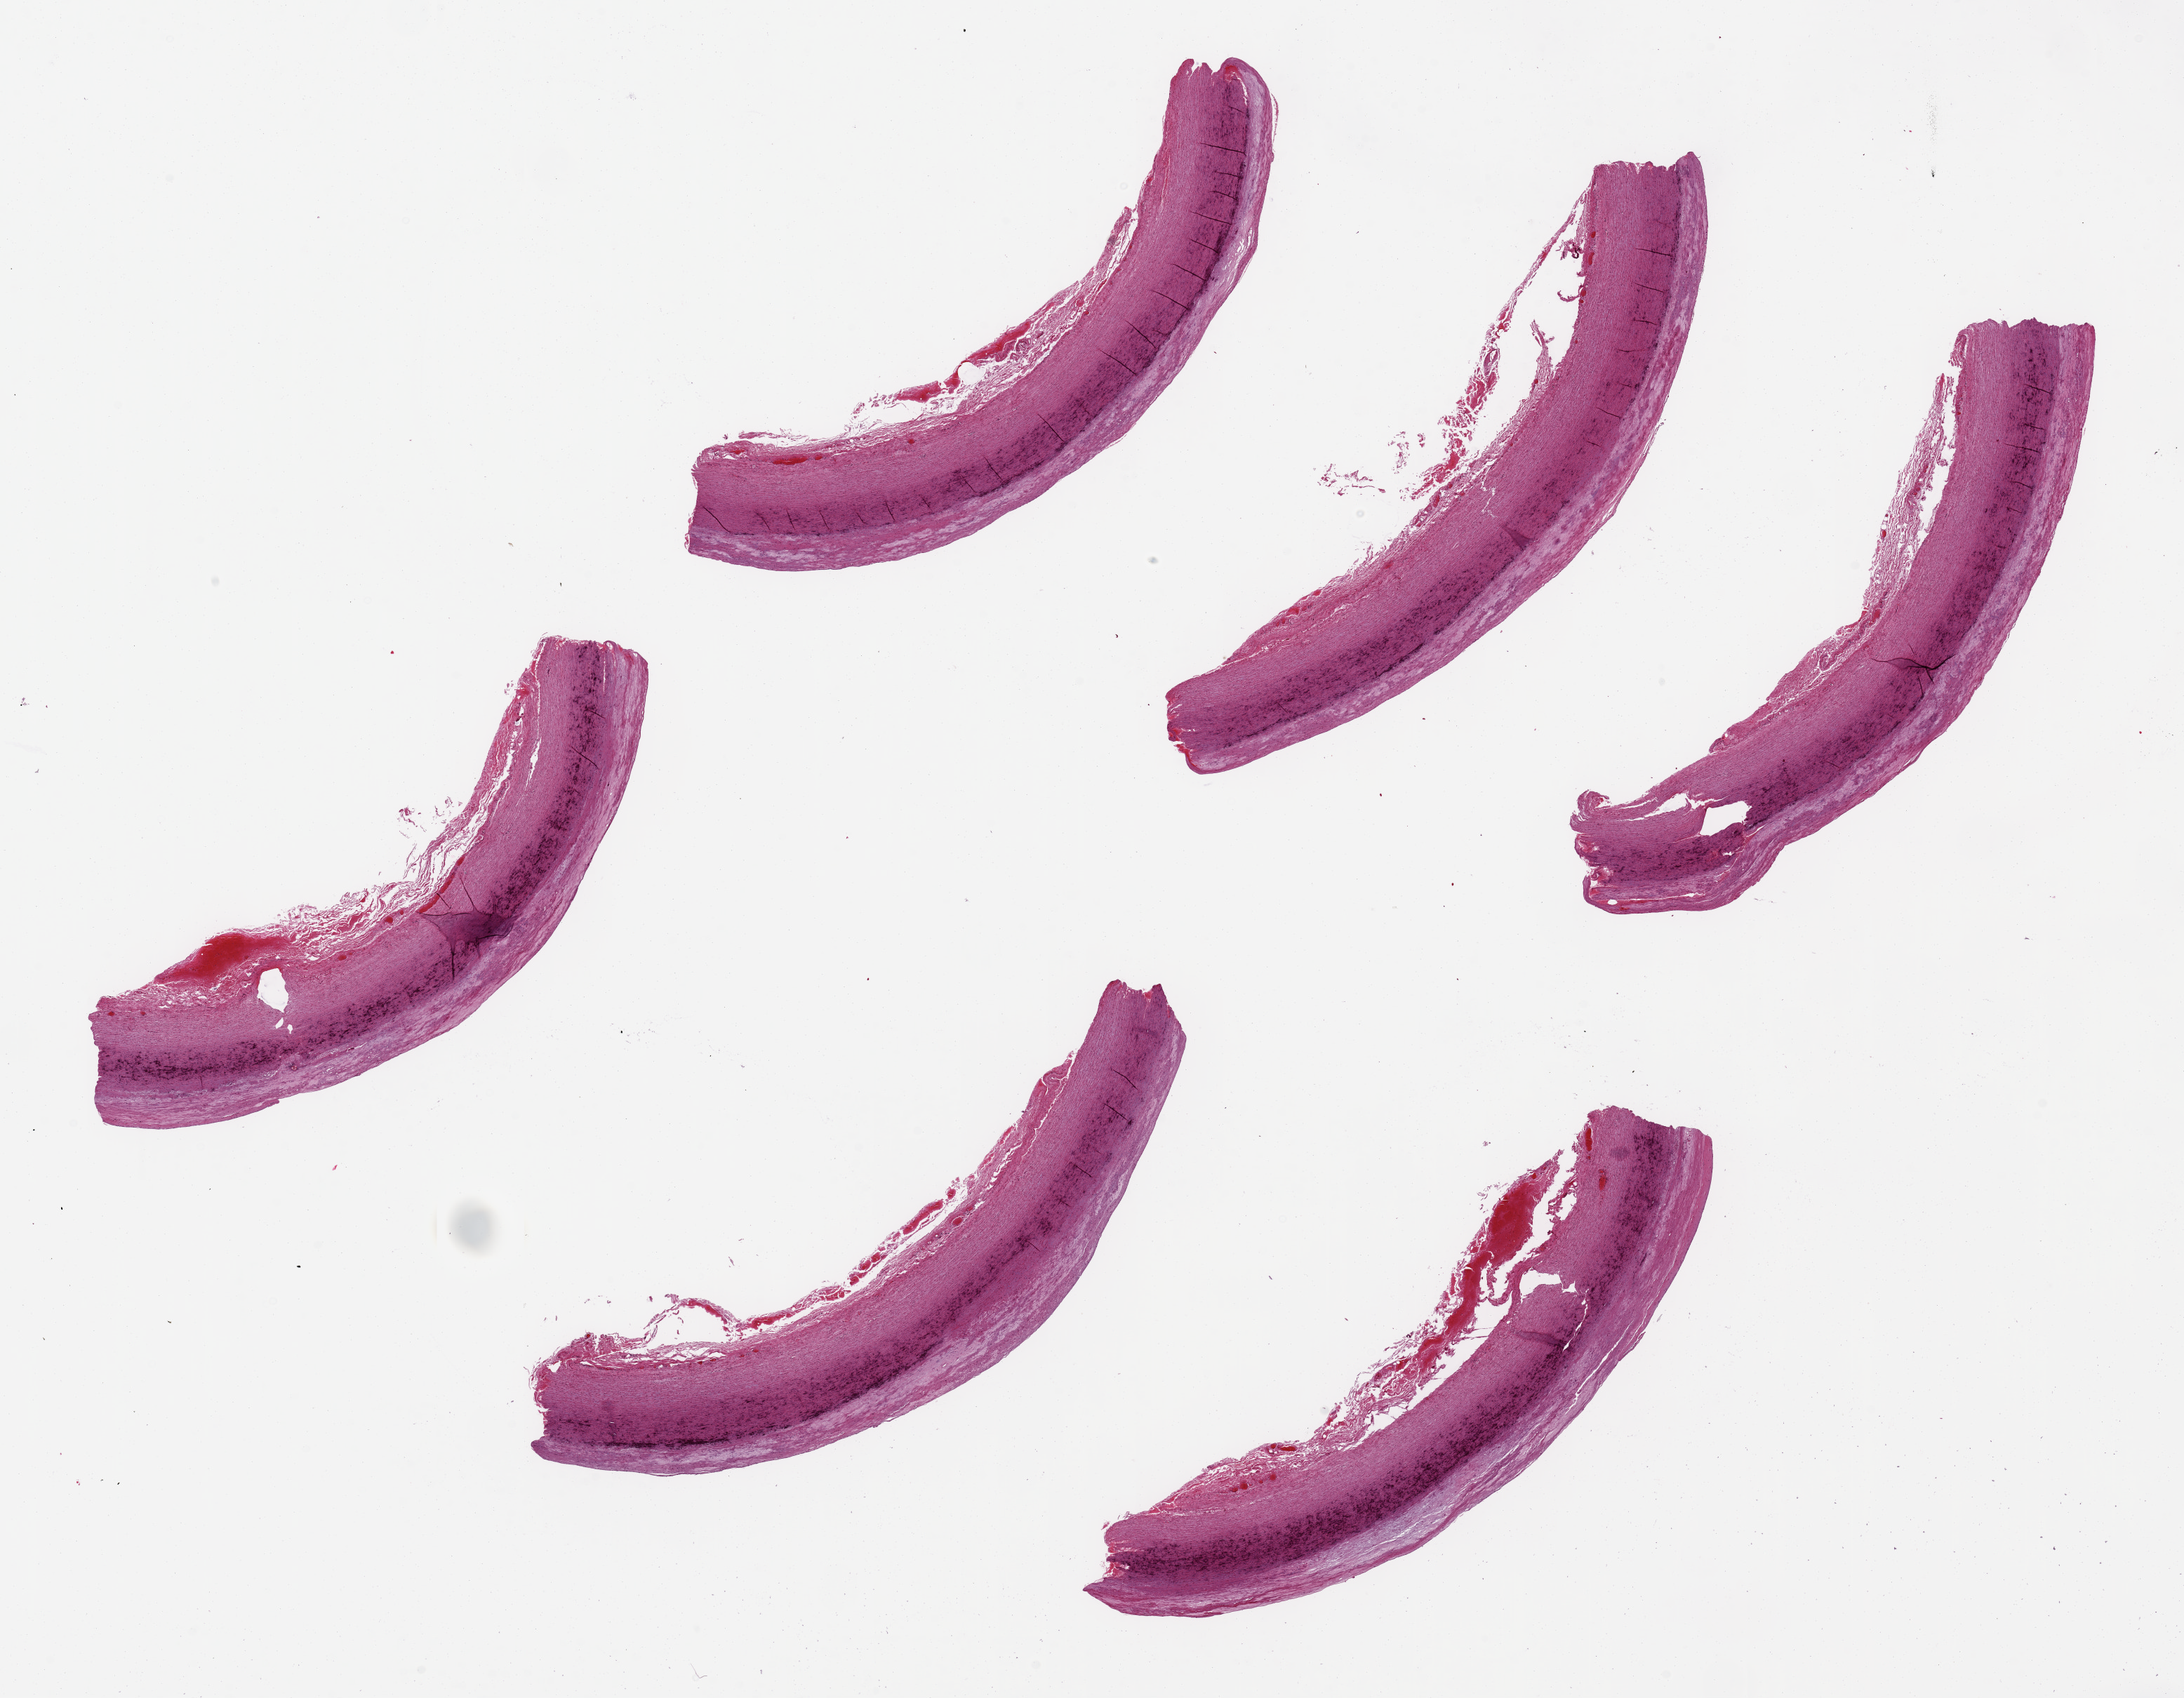
Digitized haematoxylin and eosin-stained section — a low-resolution overview of the entire scanned area, about 24.6 x 19.1 mm (acquisition: 20x scan), PAXgene-fixed paraffin-embedded (PFPE) section, target tissue: aorta, tissue donor sample. Female donor.
Pathologist's review note for this sample: 6 pieces up to 8.8x1.5 mm; moderately atherosclerotic and calcified.